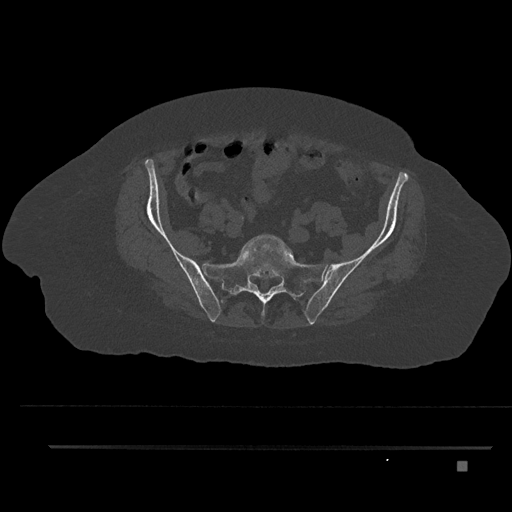
CT including the spine, one axial slice; position 4 of 797 along the scan axis; reconstruction kernel Br40s/3; 120 kVp; bone window (W 1800 / L 400 HU); 0.5 mm slice thickness; 512 × 512 image matrix, field of view 437 × 437 mm. Patient: female, 76 years. From the clinical record (not read from this slice): primary cancer: lung.
Outlined on this slice (semi-automatically segmented with operator editing):
- L5 vertebra: bounding box <242,234,293,258> (left, top, right, bottom; pixels)